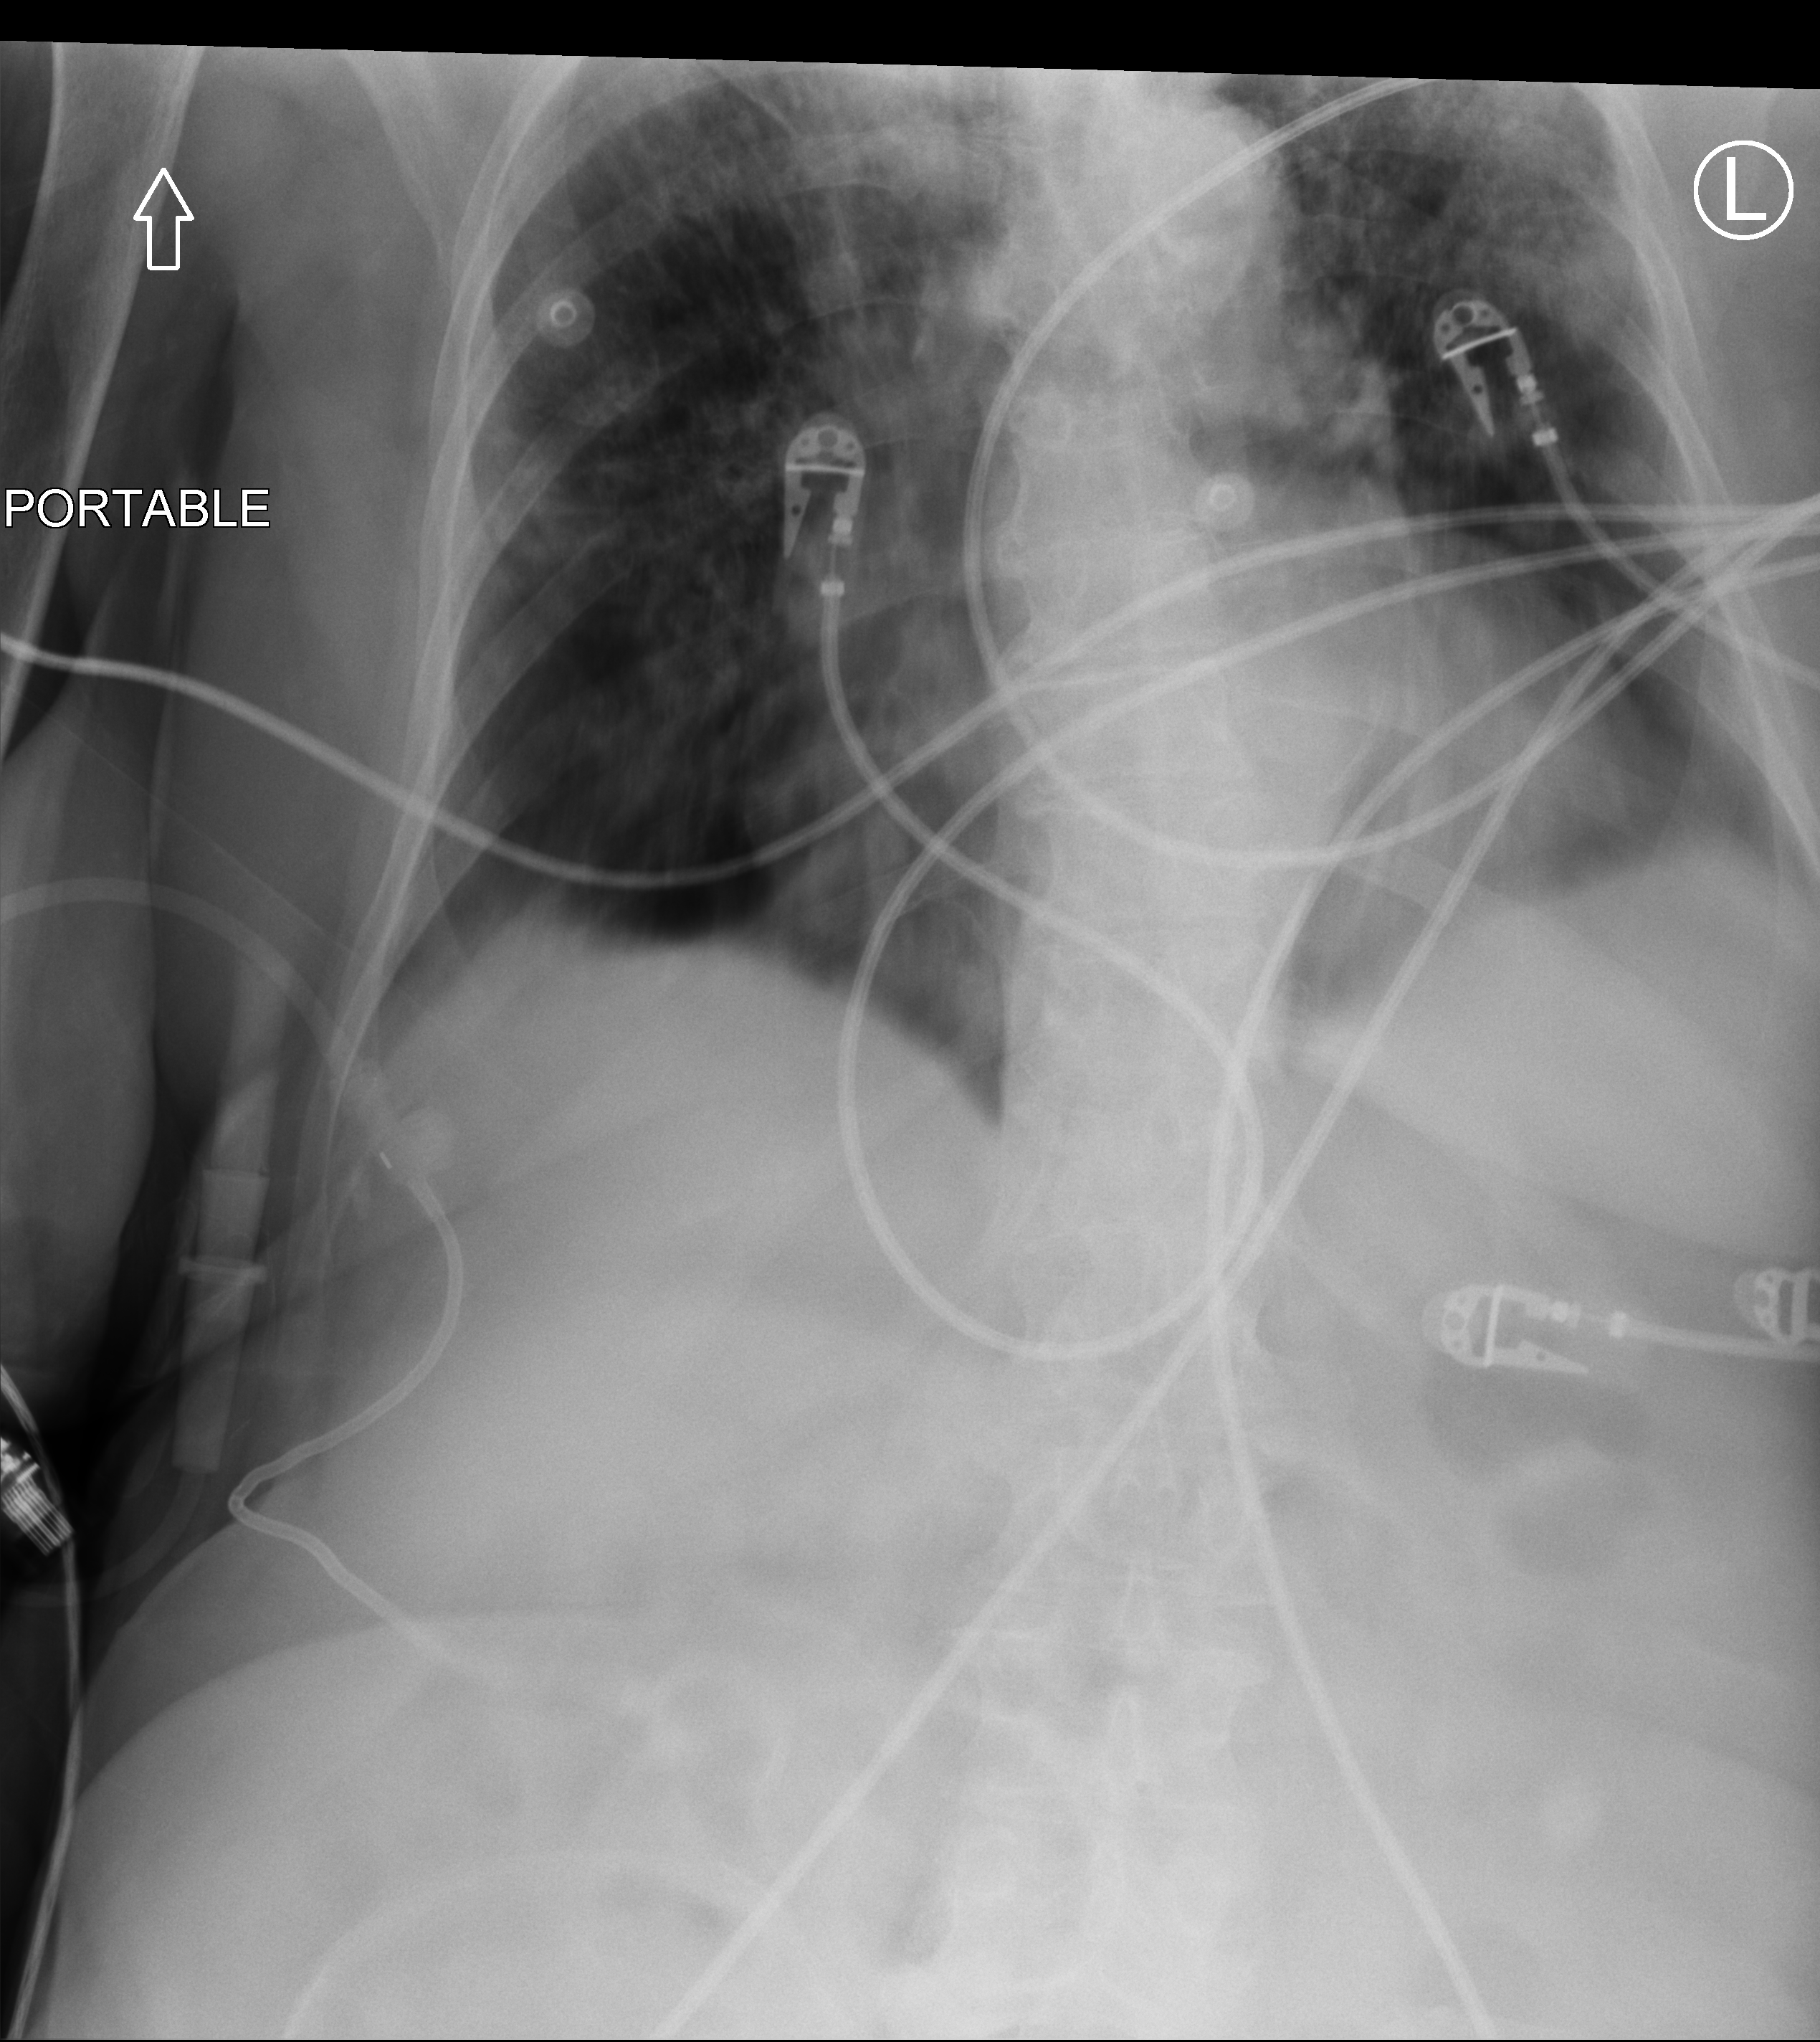
Portable abdomen radiograph. Patient hospitalised with COVID-19; female, aged 75–90 years.
Hospital-stay facts (about this admission, not read from this image; timing relative to this image not recorded):
- hypertension (admission record): yes
- admitted to intensive care during this hospital stay: no
- mechanically ventilated during this hospital stay: no